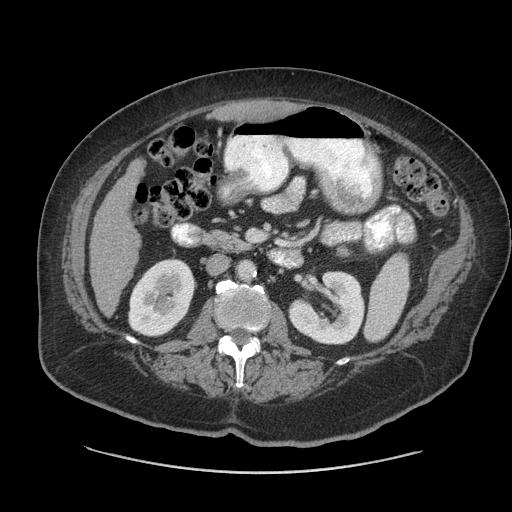
Contrast-enhanced abdominal CT (liver protocol), one axial slice; slice 20 of 91 in the series (ordered by position); reconstruction kernel STANDARD; 140 kVp; soft-tissue window (W 400 / L 40 HU); 512 × 512 image matrix. Case-level facts recorded for this patient, not image findings: diagnosis: hepatocellular carcinoma (patient treated with transarterial chemoembolisation; whether this scan precedes or follows treatment is not stated here); TNM stage (as recorded): Stage-I; Child-Pugh class: A; tumour differentiation: well differentiated.
Annotated regions visible in this slice (semi-automatic segmentation, software-assisted and operator-edited):
- liver parenchyma outside the tumour (the mass and vessels are separate outlines, so this box may not span the whole liver): bounding box [x1, y1, x2, y2] px = [90, 160, 144, 316]